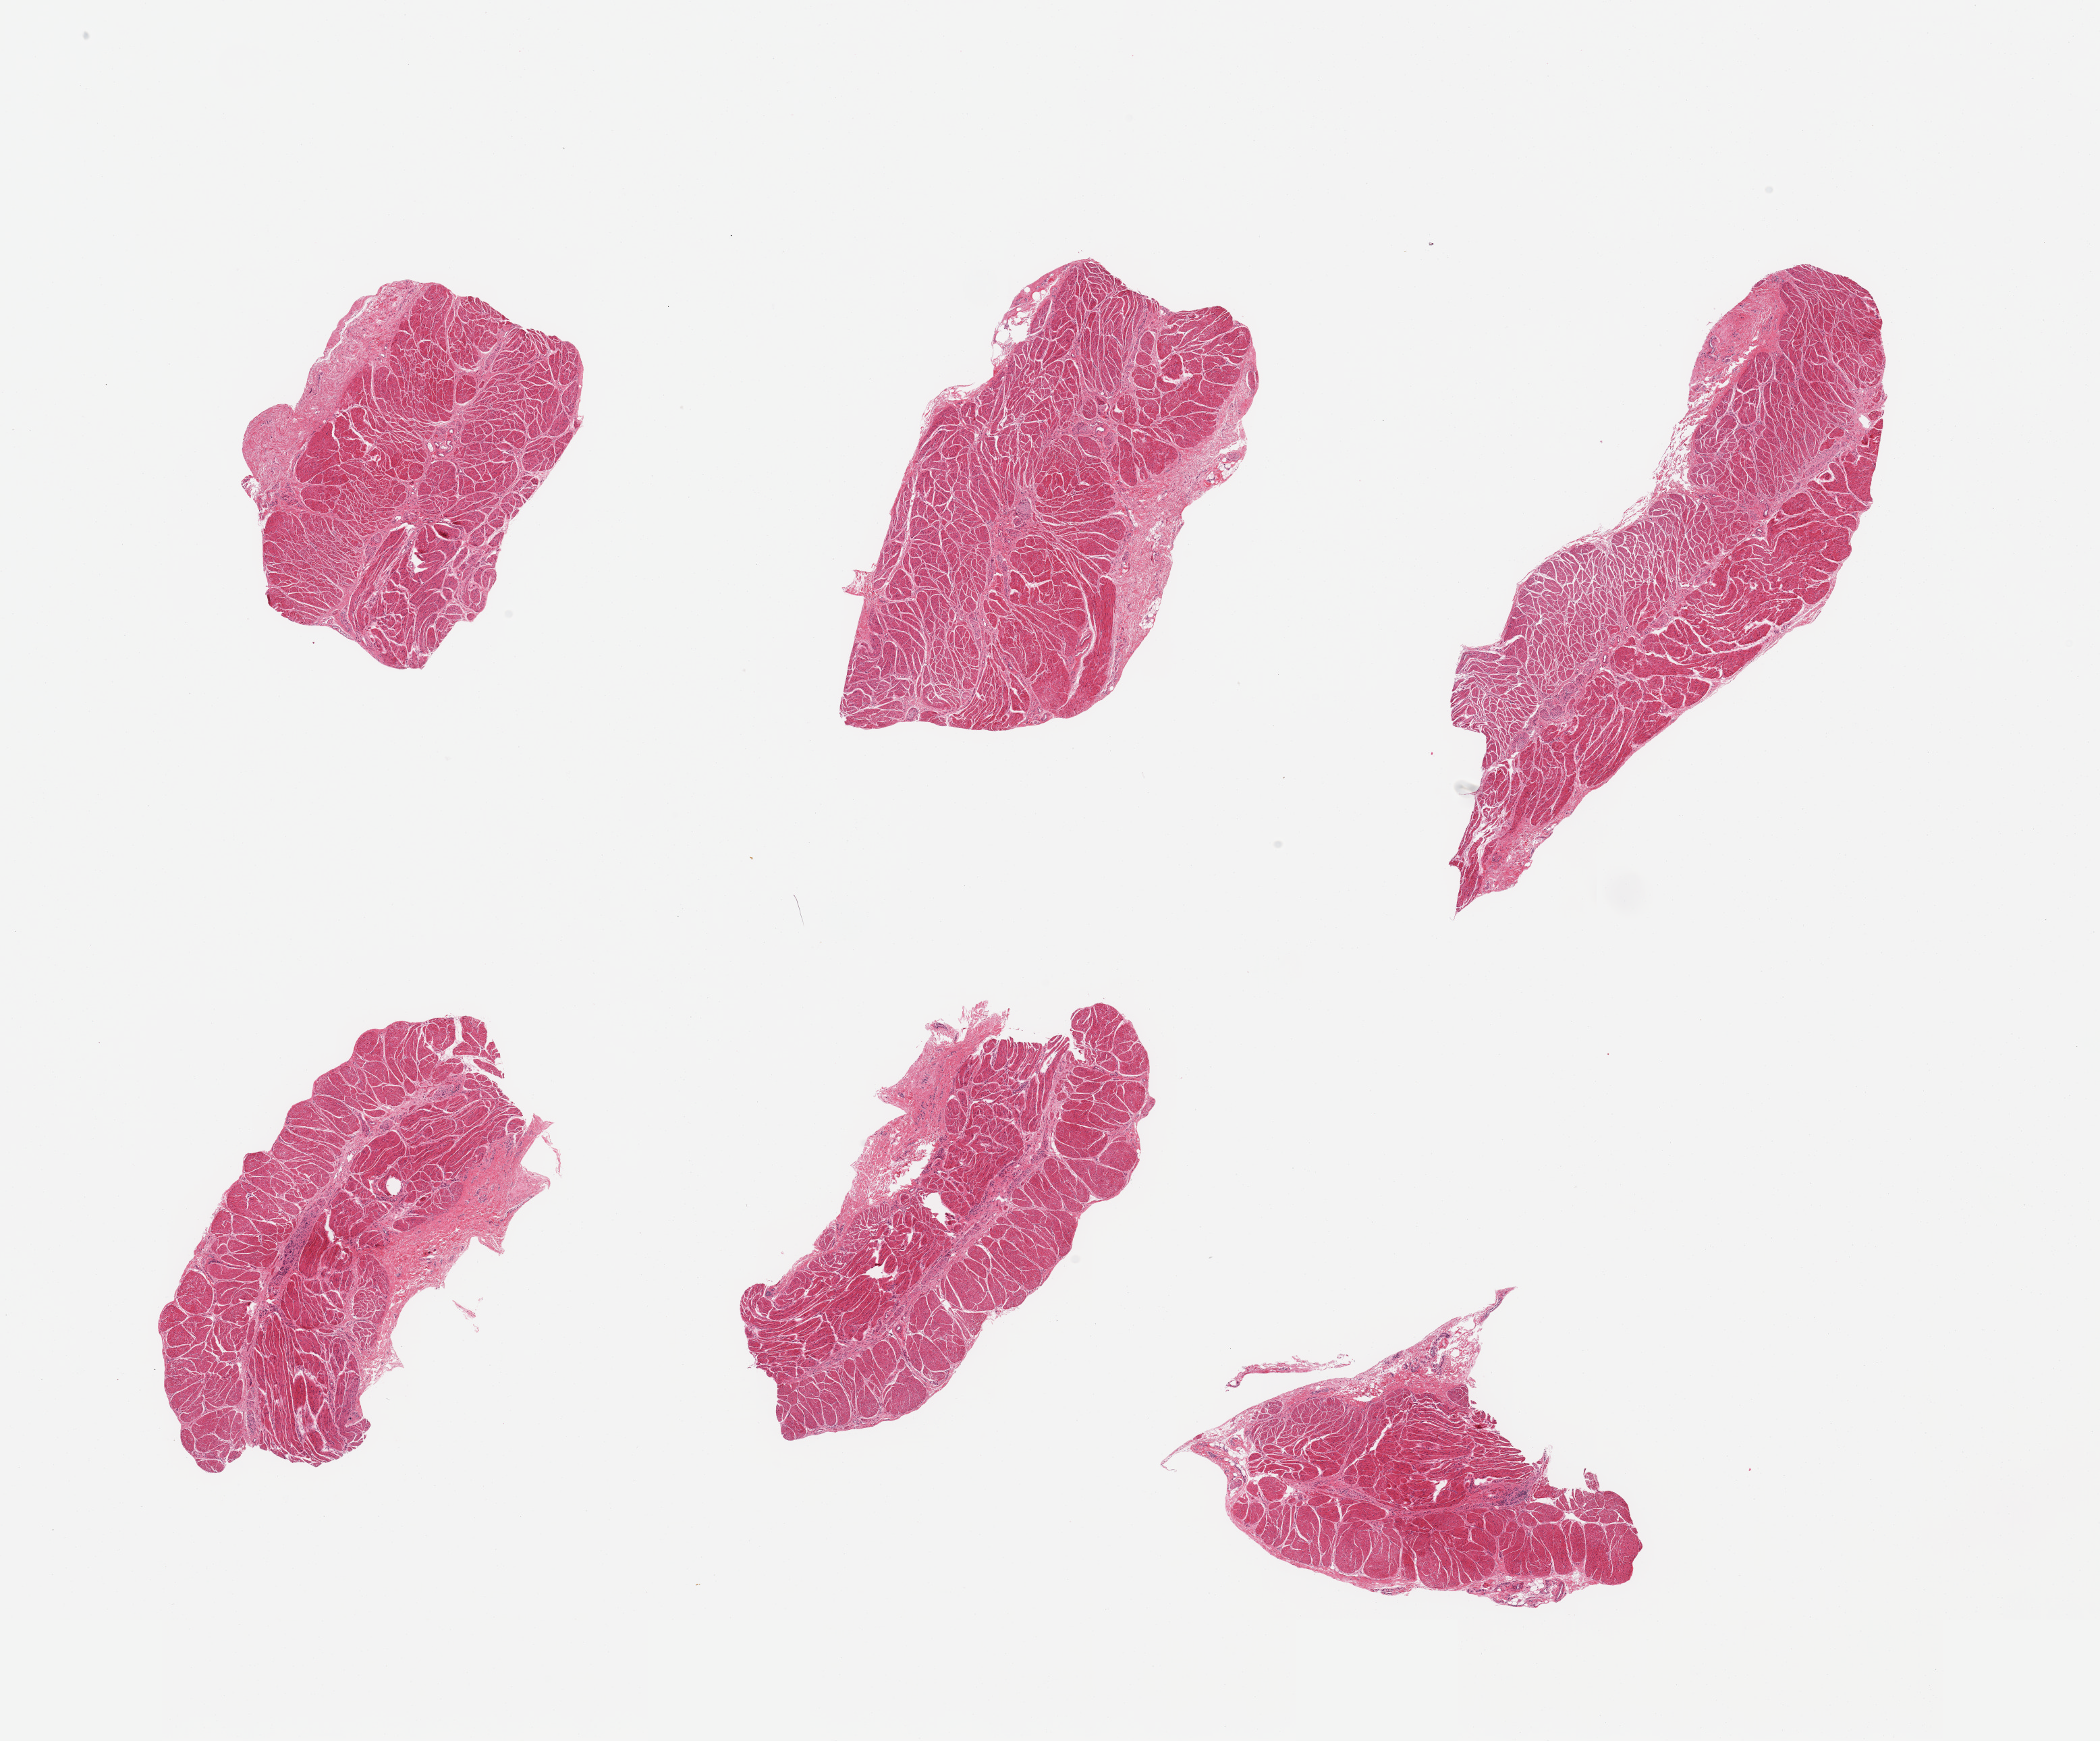
Hematoxylin and eosin (H&E) whole-slide image, a low-resolution overview of the entire scanned area, about 24.6 x 20.4 mm, PAXgene-fixed, paraffin-embedded tissue, section of gastroesophageal junction (target tissue), donor tissue sample.
Reviewer comment on this tissue sample: 6 pieces; target muscularis.